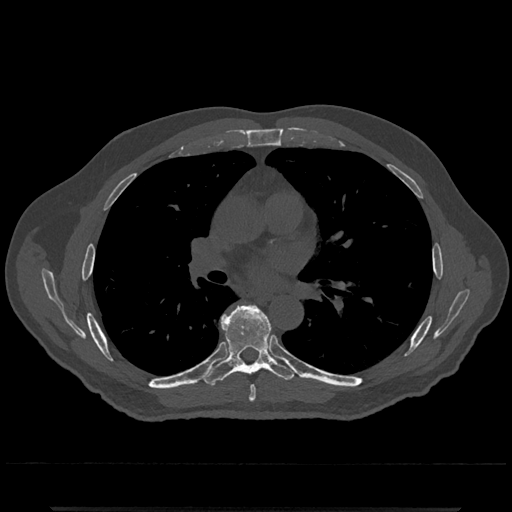
CT including the spine, one axial slice. Slice 737 of 797 in the series (ordered by position). 120 kVp. Bone window (W 1800 / L 400 HU). 512 × 512 image matrix. Male patient, age 67 years. Case-level facts recorded for this patient, not image findings: primary cancer: prostate.
Structures marked on this image (semi-automatic segmentation, software-assisted and operator-edited):
- T6 vertebra: bounding box [x1, y1, x2, y2] px = [227, 314, 256, 402]
- T7 vertebra: [202, 304, 296, 386]